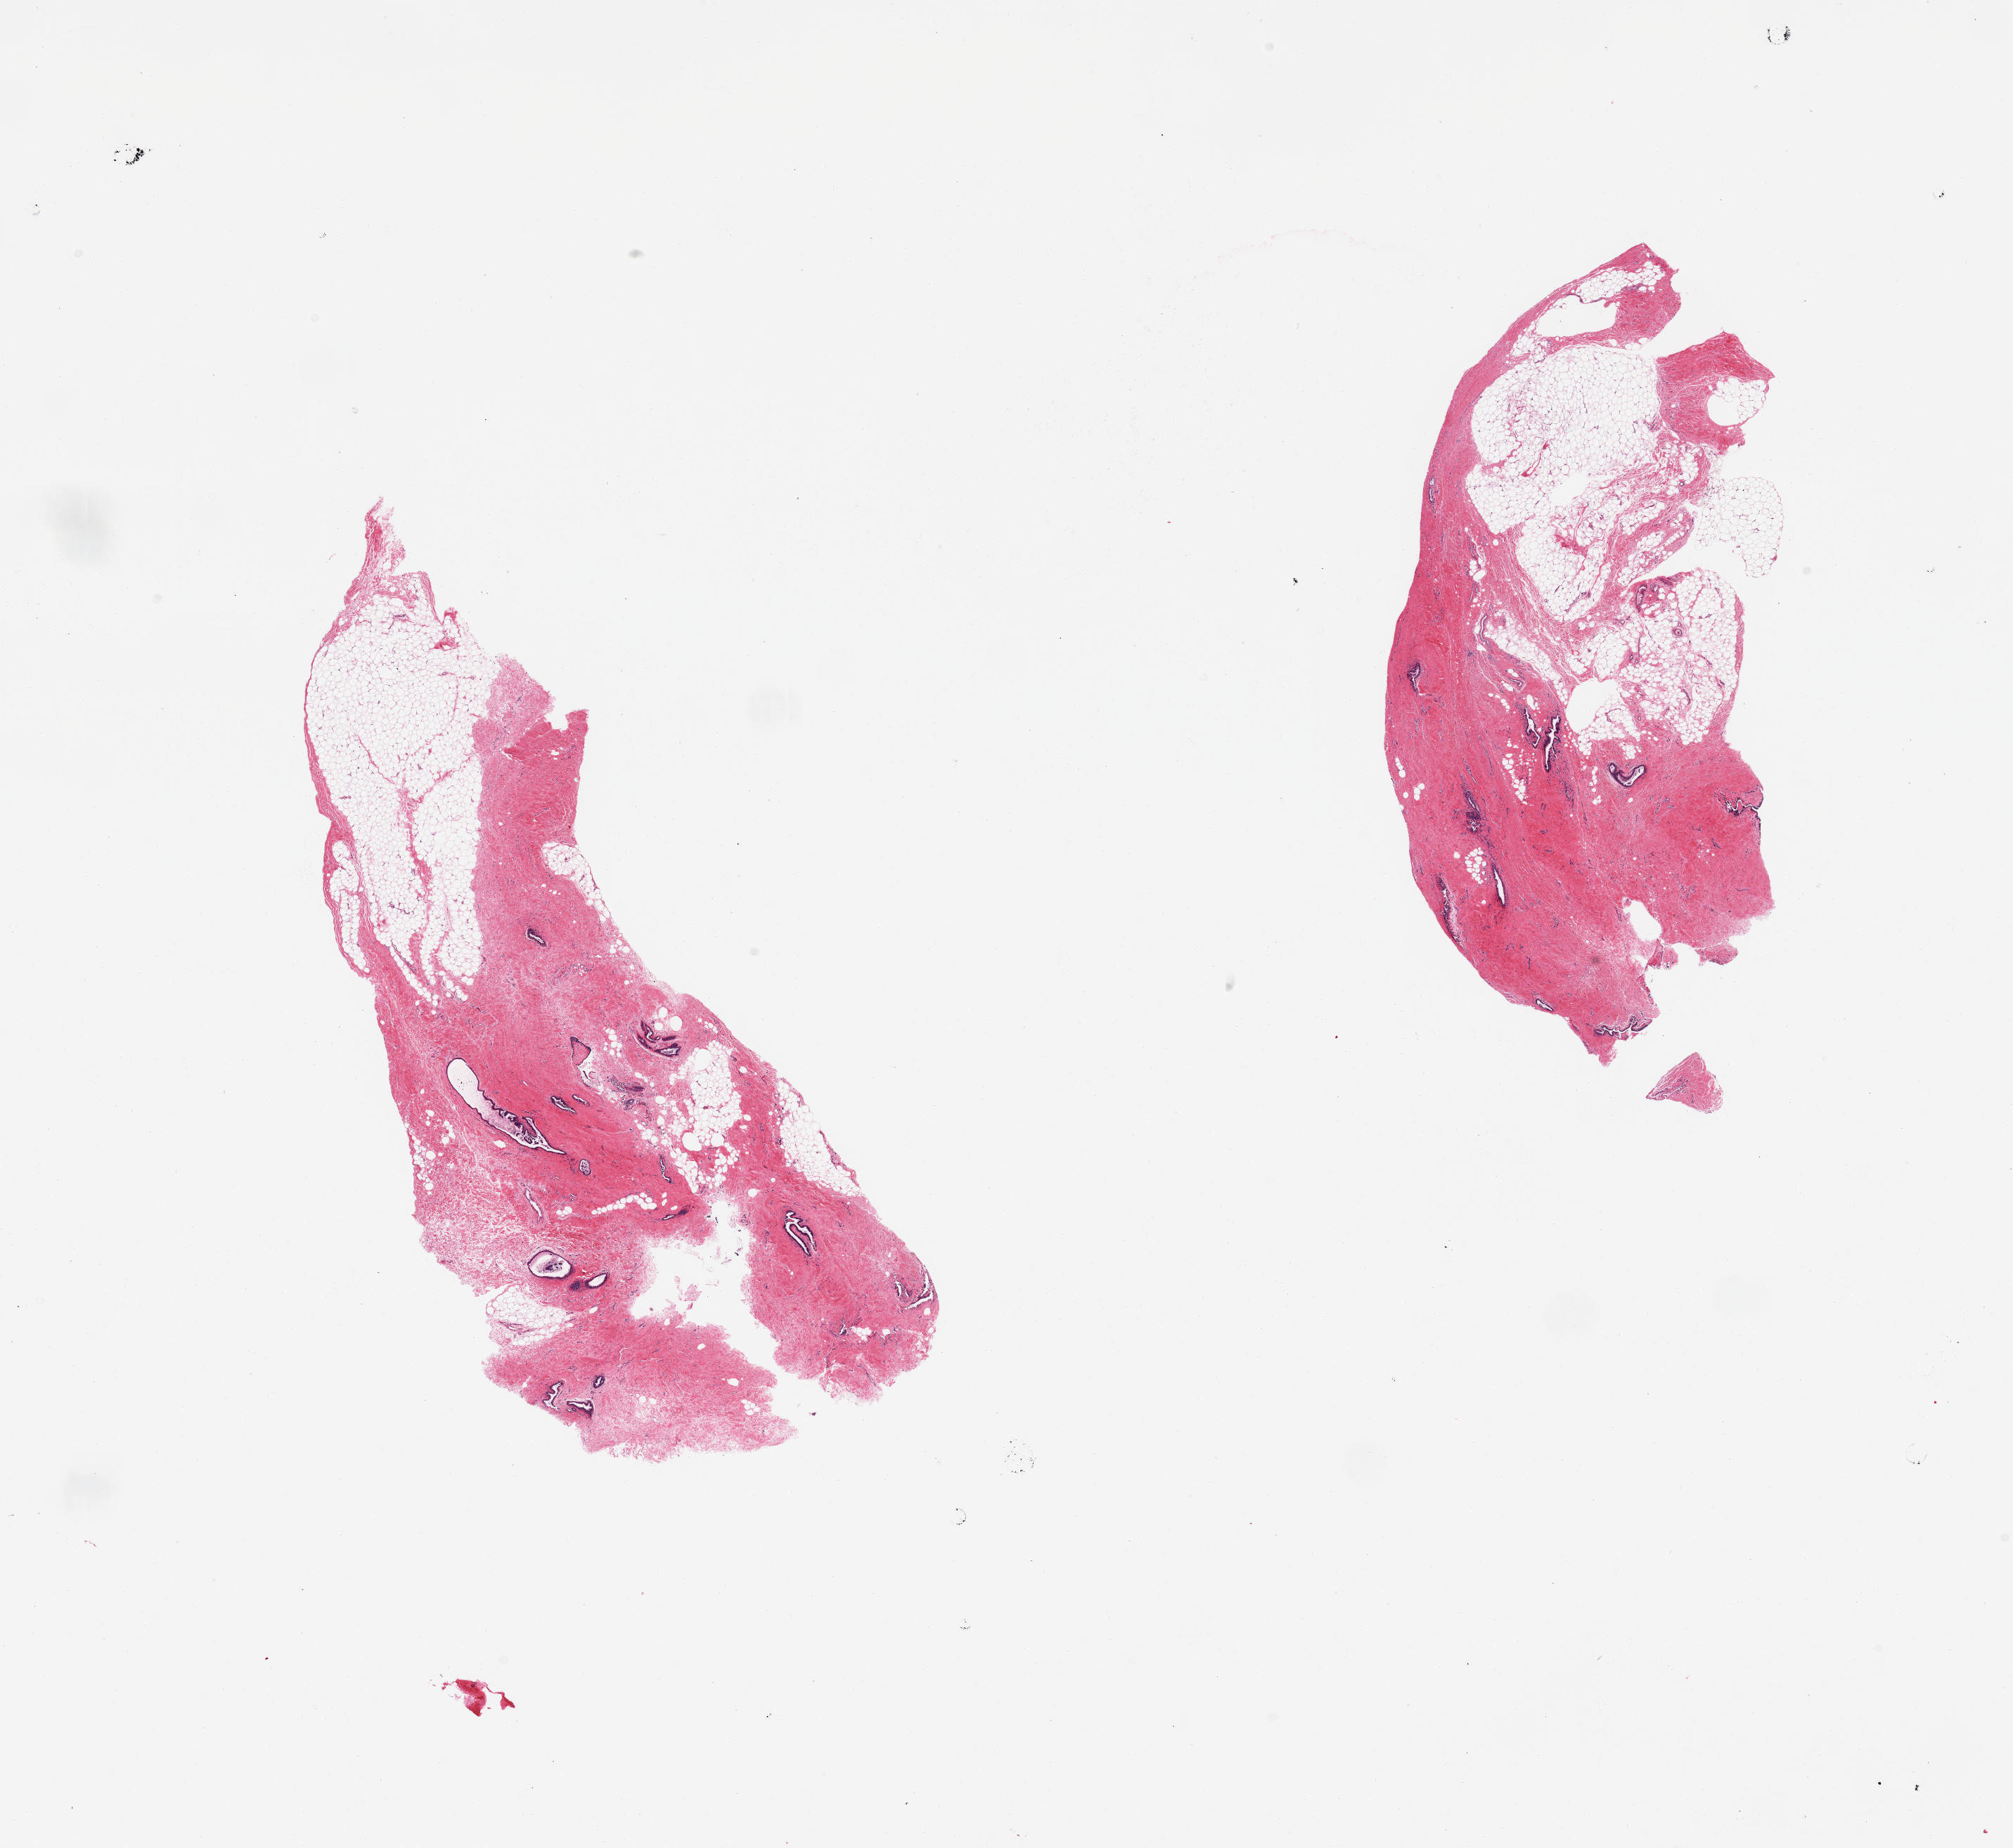
Whole-slide image, haematoxylin and eosin stain, brightfield, shown as a low-resolution overview of the whole scanned area (about 22.6 x 20.8 mm). PAXgene-fixed paraffin-embedded (PFPE) section. Section of breast (target tissue). Donor tissue sample. Donor: male.
Reviewer comment on this tissue sample: 2 pieces; adipose tissue and gynecomastoid ductal and stromal hyperplasia.